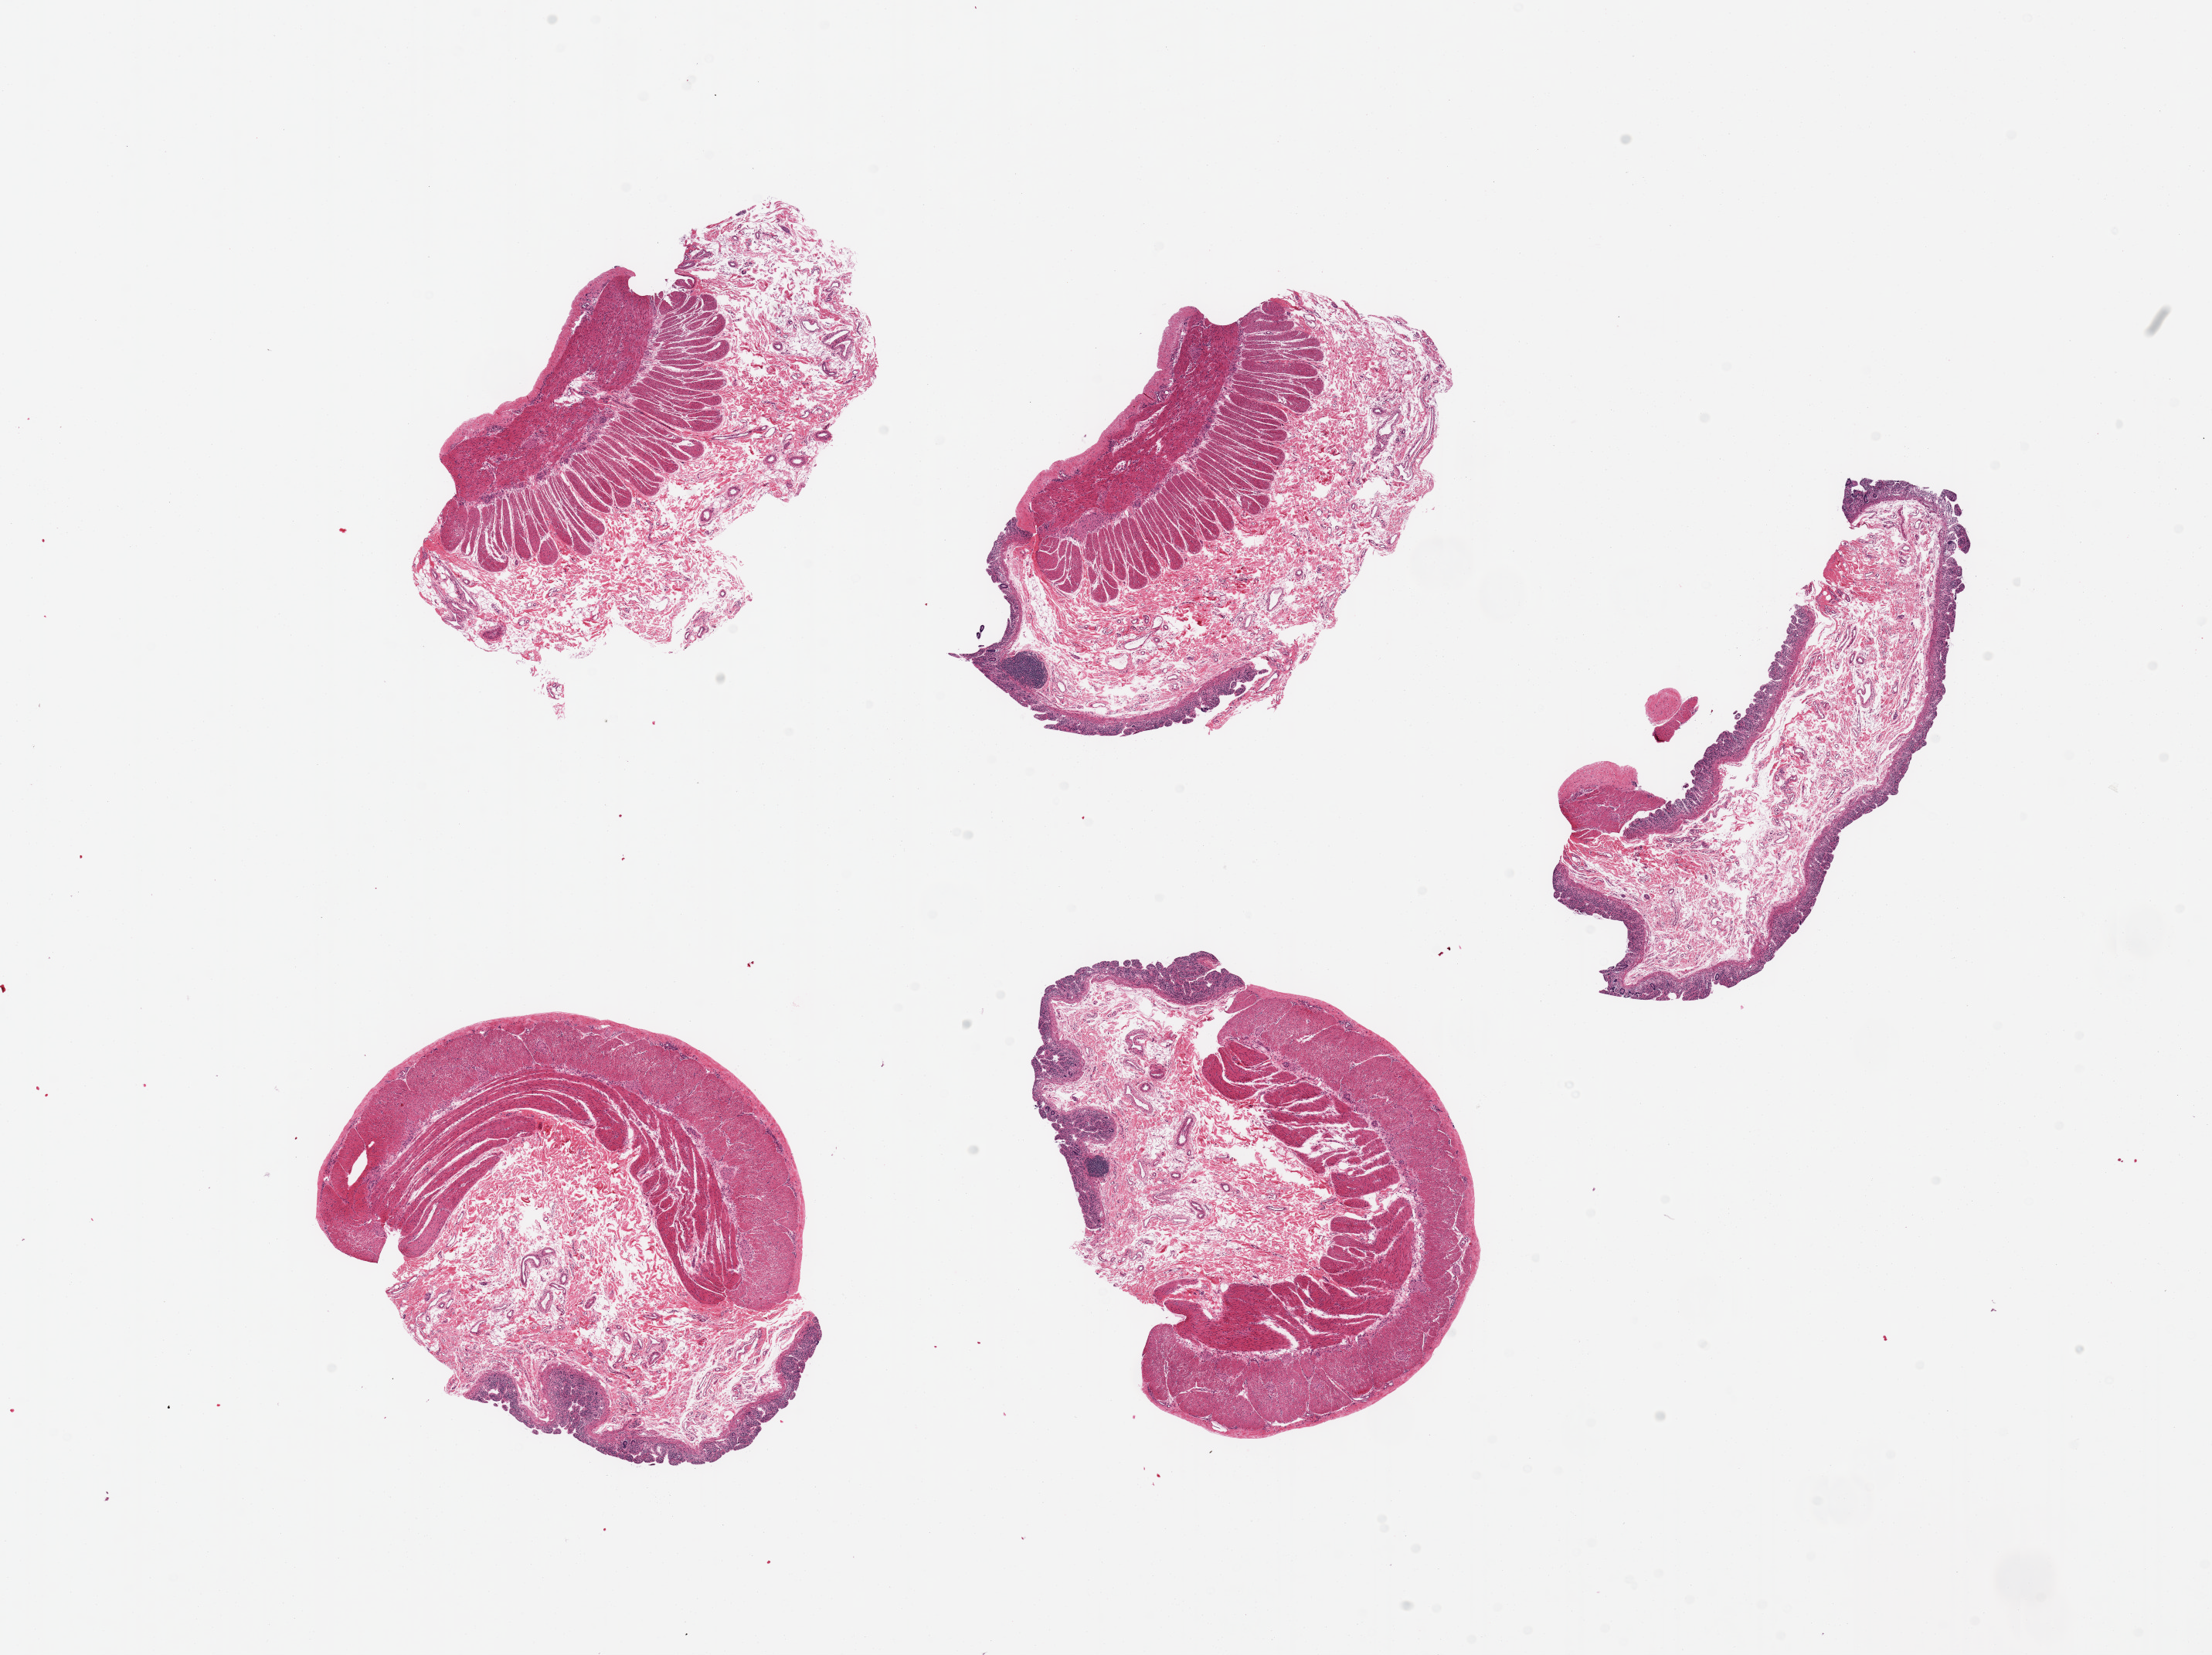
Whole-slide image, haematoxylin and eosin stain, brightfield — a low-resolution overview of the entire scanned area, about 22.6 x 16.9 mm (acquisition: 20x scan), PAXgene-fixed, paraffin-embedded tissue, sampled site (target tissue): ileum, tissue donor sample. Male donor.
Pathologist's review note for this sample: 5 pieces, < 1% target lymphoid aggregates present.